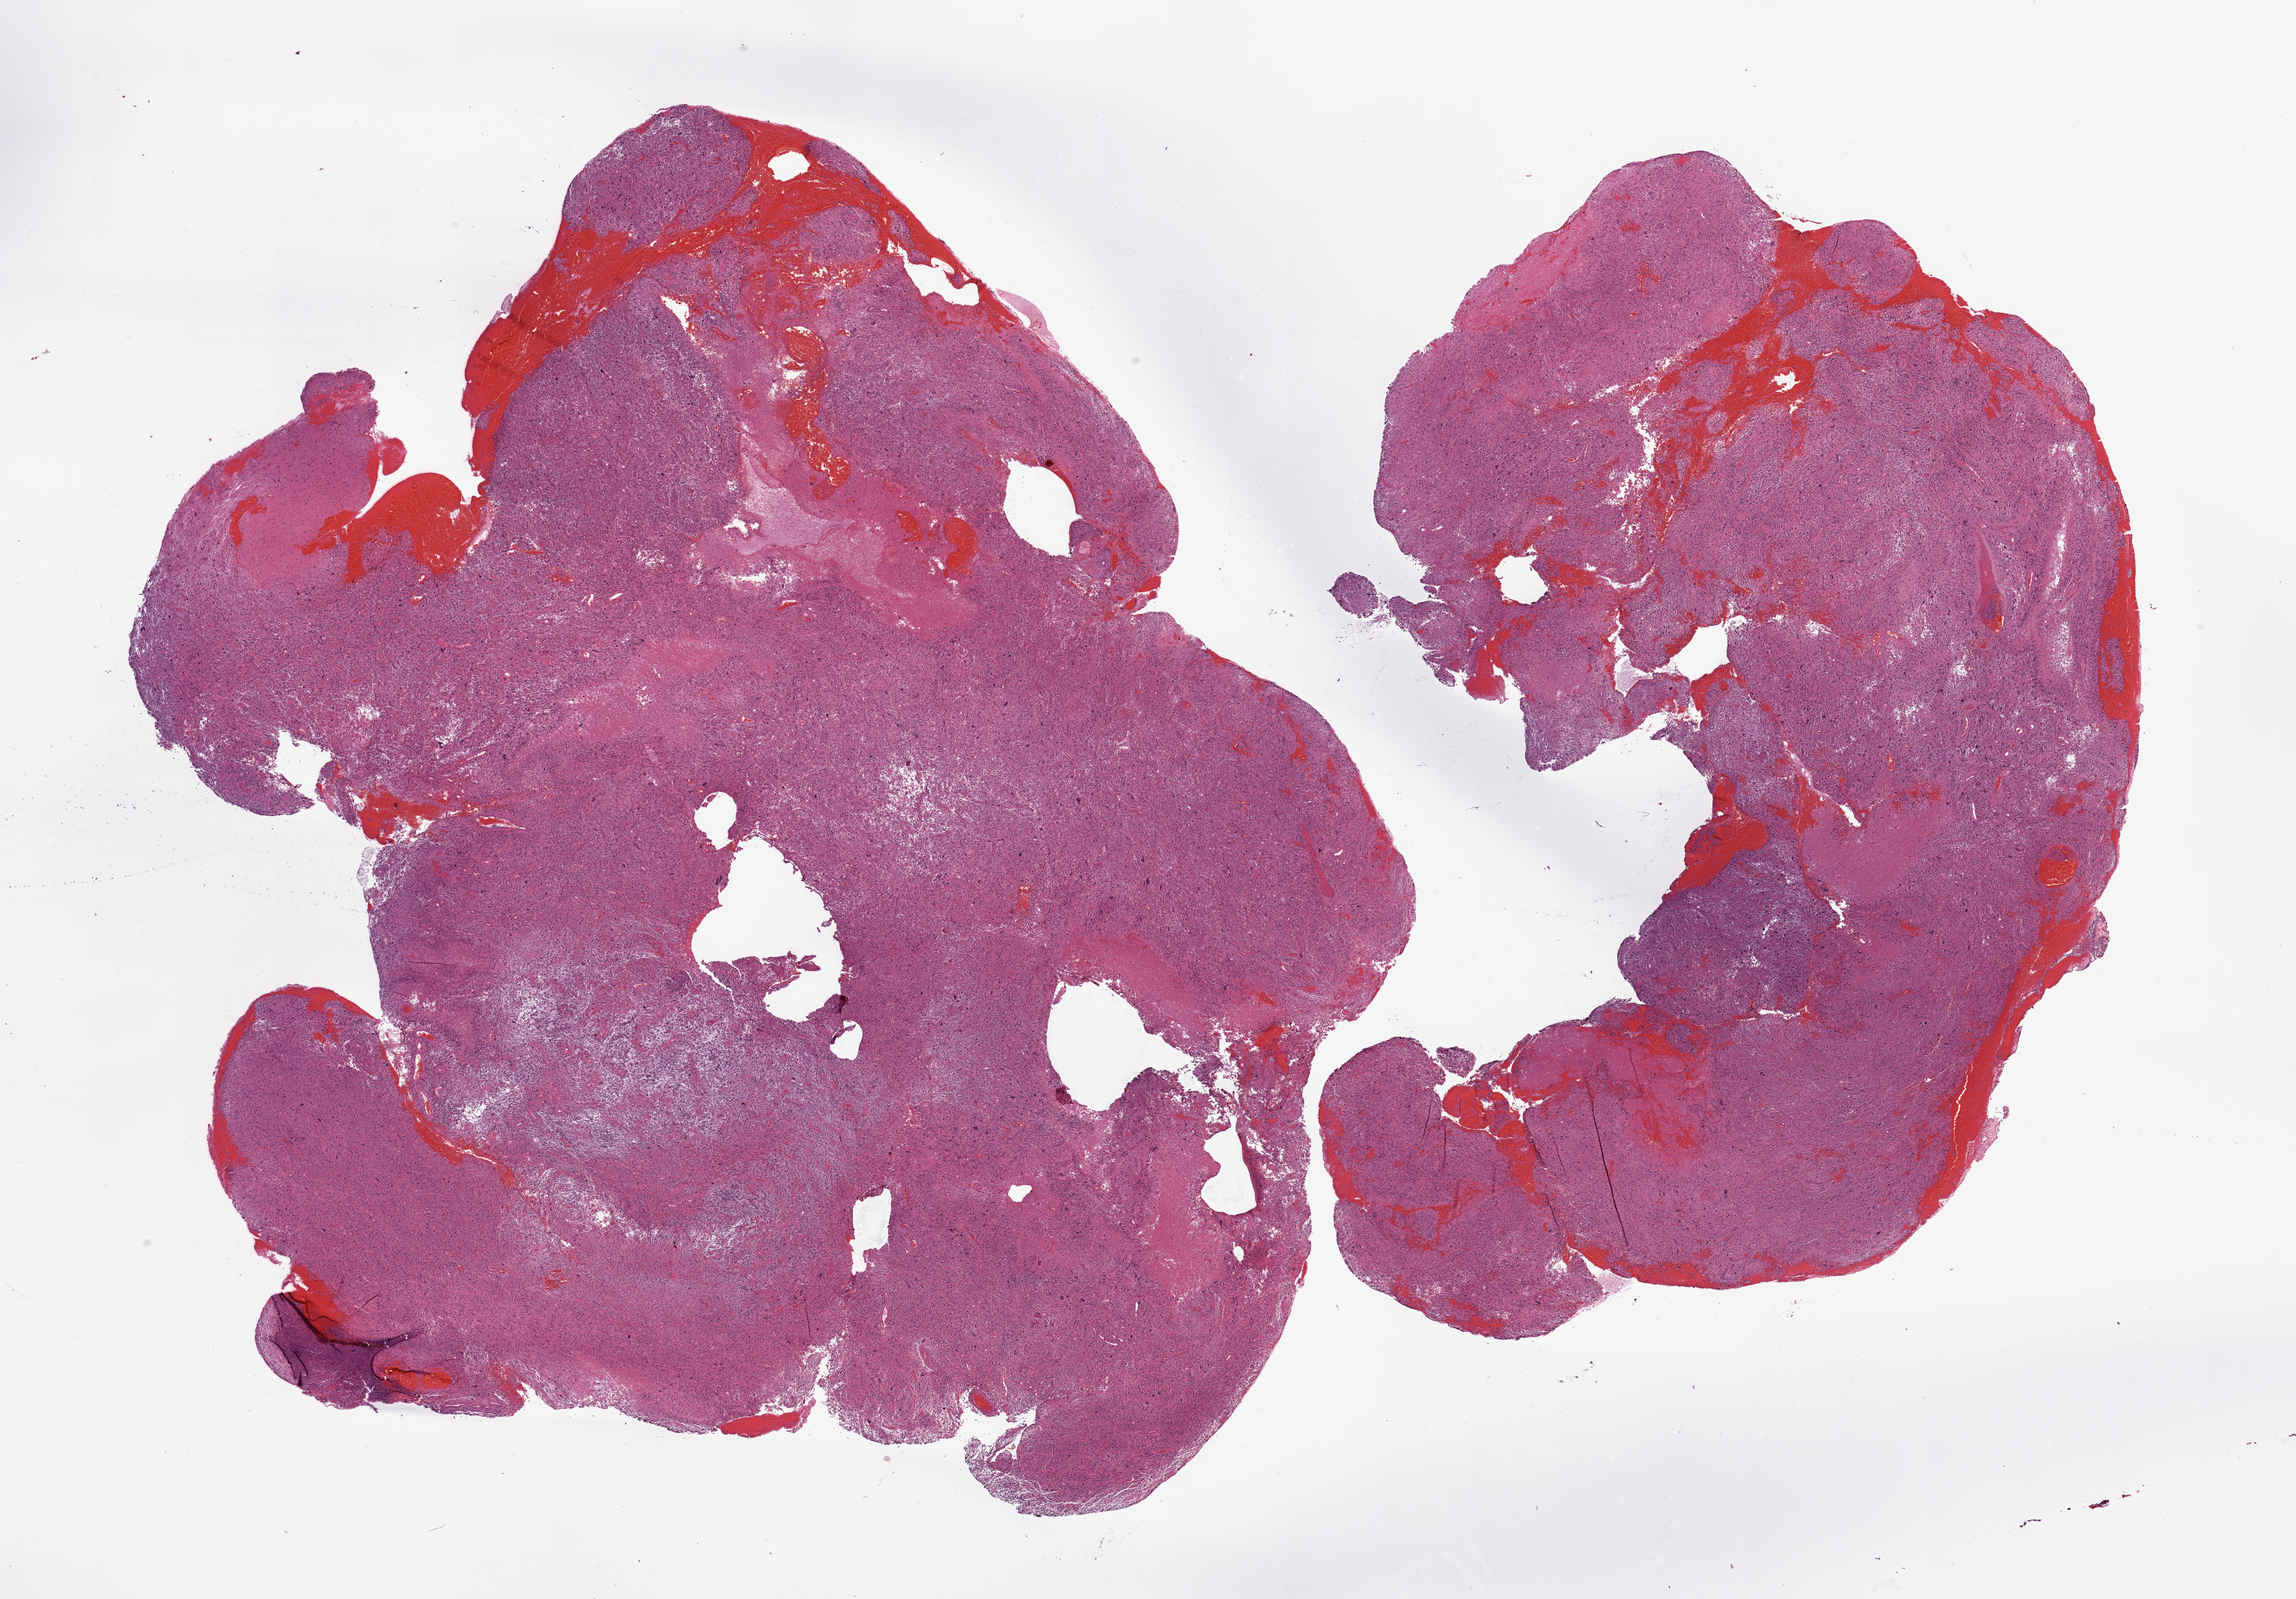
Whole-slide histology image, H&E-stained — whole scanned area (about 24.6 x 17.1 mm, slide scanned at 20x) shown as a low-resolution overview. Tumour tissue sample, brain. Patient: male, age 43 years.
Primary tumour site (as recorded): parietal lobe. Histologic diagnosis: Glioblastoma.